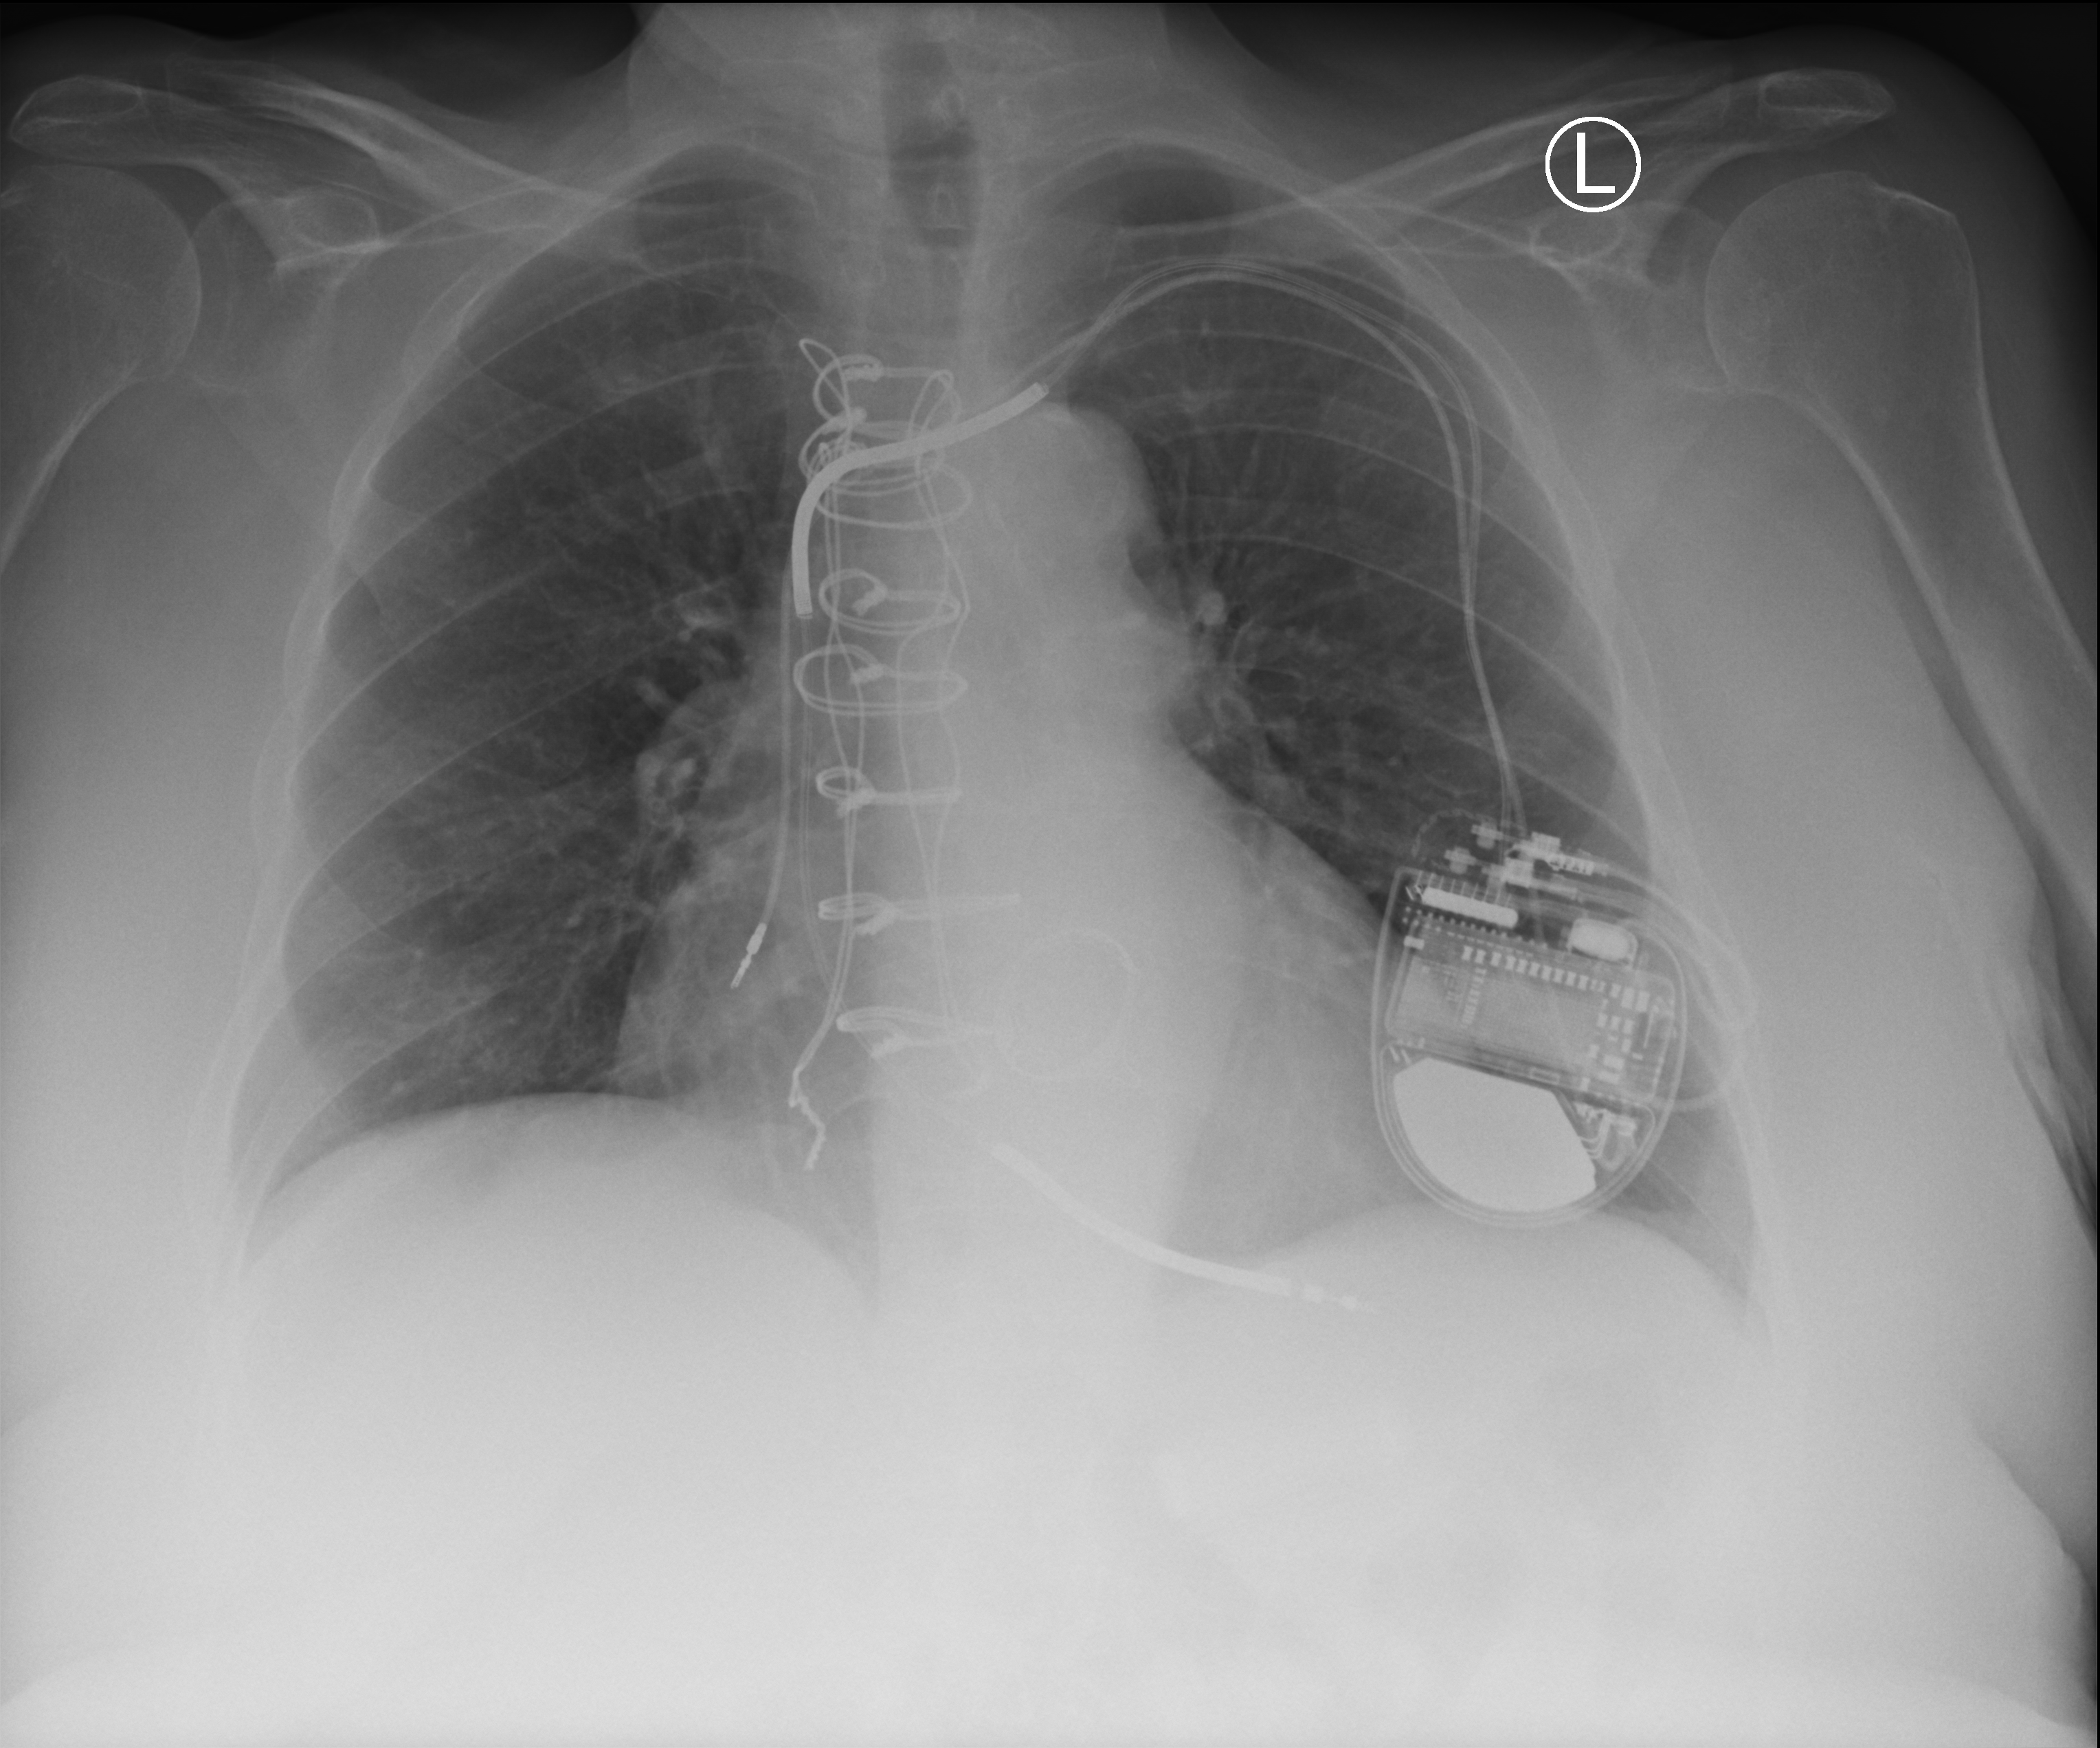
Chest X-ray; anteroposterior (AP) projection. Patient hospitalised with COVID-19; female, aged 60–74 years.
Hospital-stay facts (about this admission, not read from this image; timing relative to this image not recorded):
- admitted to intensive care during this hospital stay: yes
- mechanically ventilated during this hospital stay: no